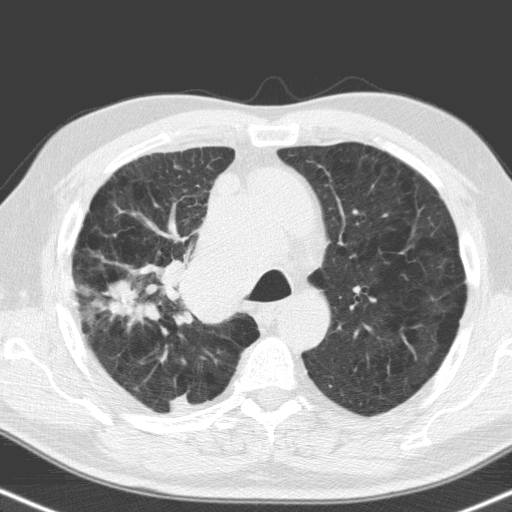
Low-dose screening chest CT, one axial slice. Position 117 of 160 along the scan axis. 120 kVp. Lung window (W 1500 / L -600 HU). 3.2 mm slice thickness. 512 × 512 image matrix, field of view 324 × 324 mm.
Outlined on this slice (outlined manually by an expert reader):
- lesion 1 (tumor, hilum of right lung): bounding box <163,224,244,322> (left, top, right, bottom; pixels)
- lesion 2 (tumor, upper lobe of right lung): <109,281,146,319>